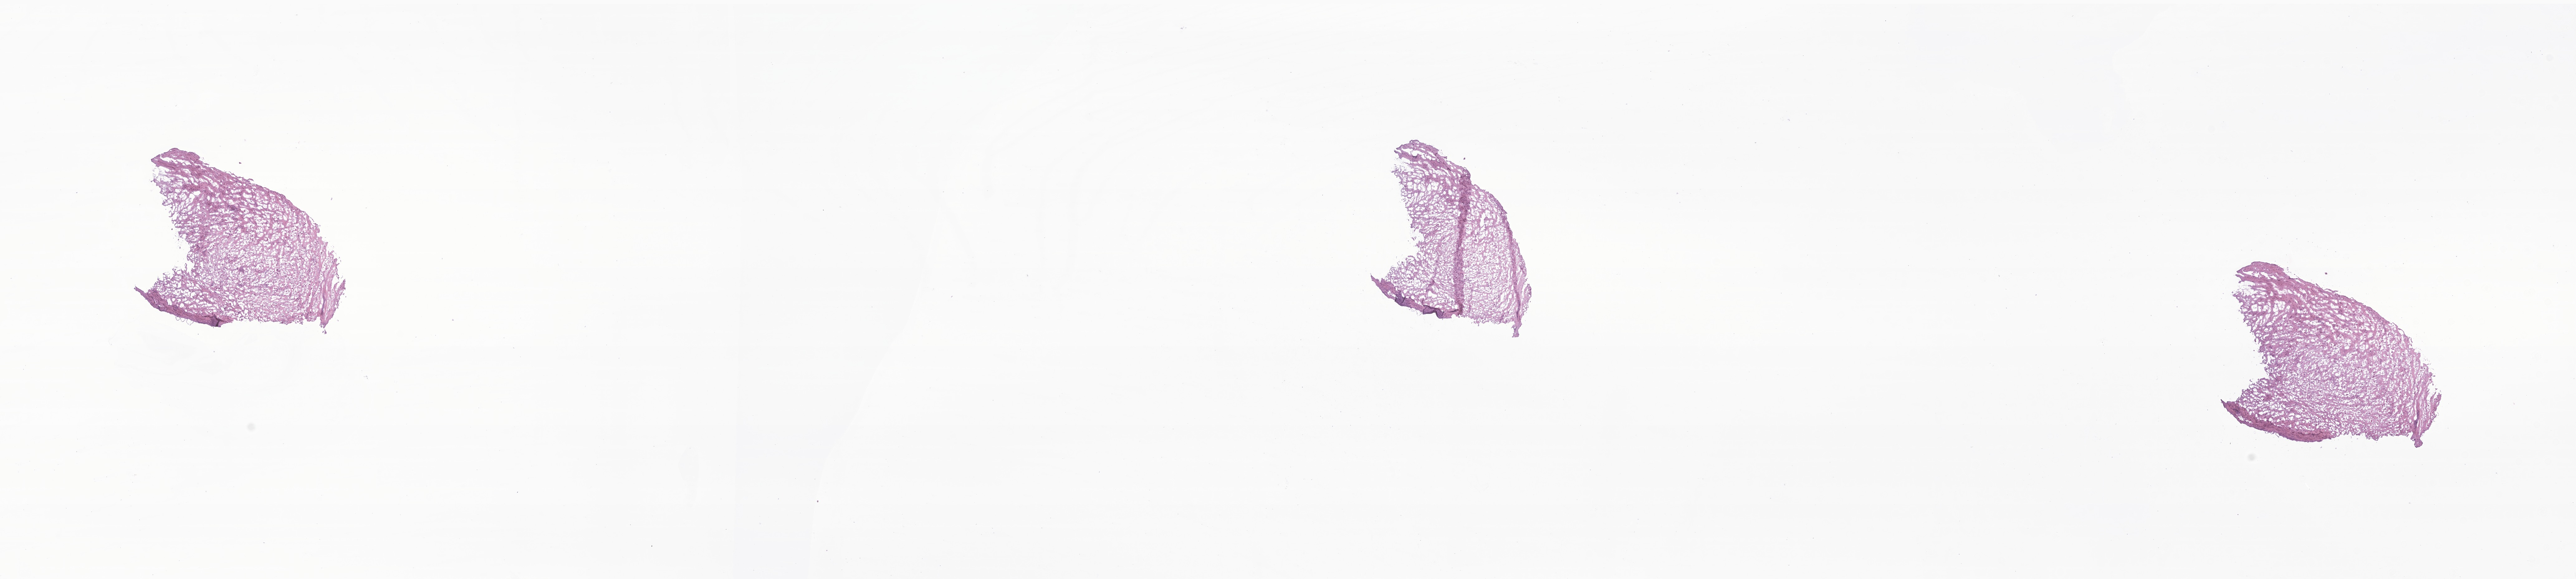
Whole-slide image, haematoxylin and eosin stain of tumor tissue from the soft tissue of trunk, whole scanned area (about 34.9 x 7.8 mm) shown as a low-resolution overview. Frozen section (OCT-embedded). Patient female; age 60 months (5 years).
Recorded diagnosis: Rhabdomyosarcoma, NOS.